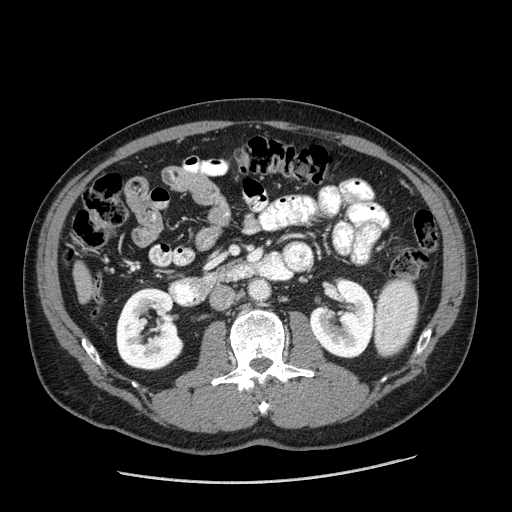
Contrast-enhanced abdominal CT (liver protocol), one axial slice; position 47 of 198 along the scan axis; one of 2 acquisitions stored at this slice position; soft-tissue window (W 400 / L 40 HU); 2.5 mm slice thickness; 512 × 512 image matrix, field of view 400 × 400 mm. Case-level facts recorded for this patient, not image findings: diagnosis: hepatocellular carcinoma (patient treated with transarterial chemoembolisation; whether this scan precedes or follows treatment is not stated here); TNM stage (as recorded): Stage-II; Child-Pugh class: A; tumour differentiation: moderately differentiated; tumour nodularity: multinodular.
Outlined on this slice (semi-automatically segmented with operator editing):
- liver parenchyma outside the tumour (the mass and vessels are separate outlines, so this box may not span the whole liver): bounding box (x1, y1, x2, y2) in pixels: (74, 262, 94, 302)